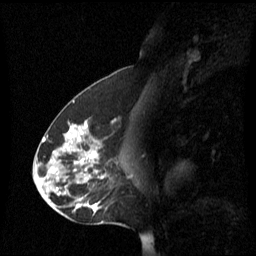
Breast MRI (dynamic contrast-enhanced), one sagittal slice. Dynamic contrast-enhanced series, image 2 of 3 at this slice position (ordered by acquisition). 1.5 T. TE 4.2 ms, TR 8.4 ms. 2.2 mm slice thickness. 256 × 256 image matrix, field of view 240 × 240 mm. Patient: female, 45 years. From the clinical record (not read from this slice): setting: breast cancer imaged before/during neoadjuvant chemotherapy; receptor status: HR-positive, HER2-negative.
Structures marked on this image (semi-automatic segmentation, software-assisted and operator-edited):
- analysis volume of interest (the breast-tissue region the enhancement analysis was run in; not a lesion): bounding box <38,120,129,221> (left, top, right, bottom; pixels)
- tumour enhancement mask (voxels above the 70 % enhancement threshold inside the analysis volume of interest): <52,122,105,211>